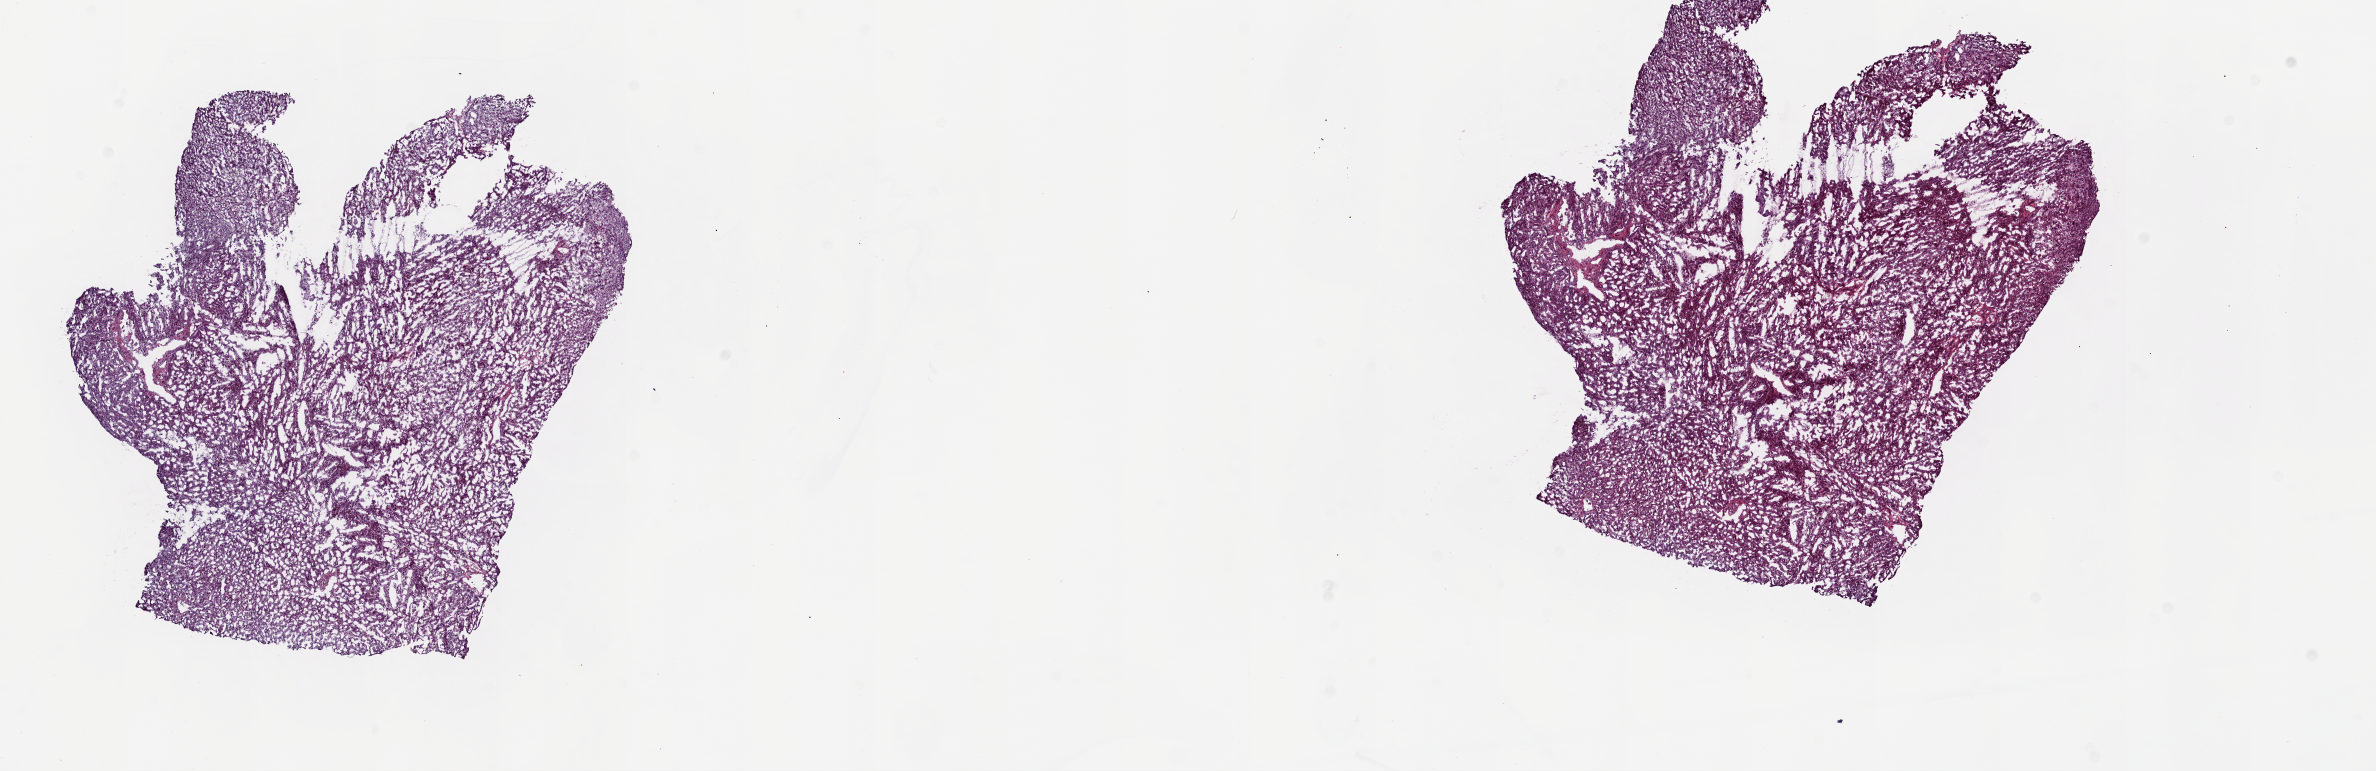
Whole-slide histology image, H&E — a low-resolution overview of the entire scanned area, about 18.8 x 6.1 mm (slide scanned at 20x); frozen section from the top of the tissue portion; liver, solid tissue normal (non-tumour tissue) sample. Male, age 71 years at initial diagnosis. Slide review estimates, as recorded: tumour cells 0%, tumour nuclei 0%, normal cells 100%, stromal cells 0%, necrosis 0%. Infiltration values recorded for this section: lymphocyte infiltration 0%, monocyte infiltration 0%, neutrophil infiltration 0%.
This section: solid tissue normal (non-tumour) sample from the same patient. Patient diagnosis: Hepatocellular carcinoma, NOS.